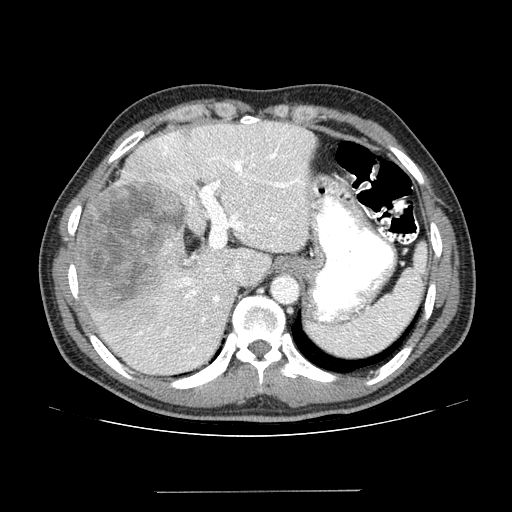
Contrast-enhanced abdominal CT (liver protocol), one axial slice; position 101 of 131 along the scan axis; reconstruction kernel STANDARD; 100 kVp; one of 2 acquisitions stored at this slice position; soft-tissue window (W 400 / L 40 HU); 2.5 mm slice thickness; 512 × 512 image matrix. Case-level facts recorded for this patient, not image findings: diagnosis: hepatocellular carcinoma (patient treated with transarterial chemoembolisation; whether this scan precedes or follows treatment is not stated here); TNM stage (as recorded): Stage-I; Child-Pugh class: A; tumour differentiation: poorly differentiated; tumour size: 10.3 cm.
Annotated regions visible in this slice (semi-automatically segmented with operator editing):
- liver parenchyma outside the tumour (the mass and vessels are separate outlines, so this box may not span the whole liver): bounding box [x1, y1, x2, y2] px = [74, 122, 314, 374]
- mass: [79, 181, 187, 316]
- liver vessels: [132, 125, 304, 366]